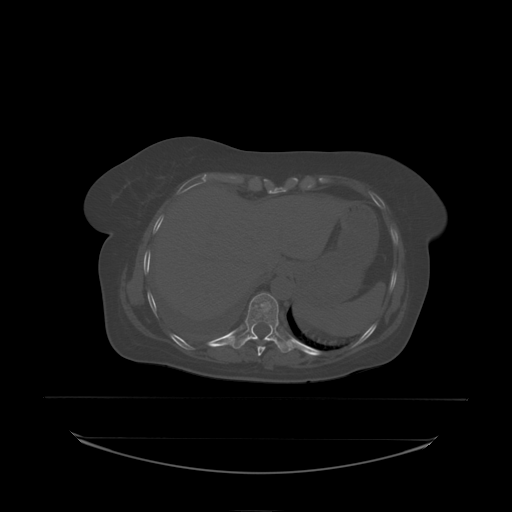
CT including the spine, one axial slice. Slice 116 of 242 in the series (ordered by position). Bone window (W 1800 / L 400 HU). 512 × 512 image matrix, field of view 500 × 500 mm. Female patient, age 53 years. Case-level facts recorded for this patient, not image findings: primary cancer: lung.
Structures marked on this image (semi-automatic segmentation, software-assisted and operator-edited):
- T10 vertebra: box from (x=241, y=293) to (x=279, y=338) px